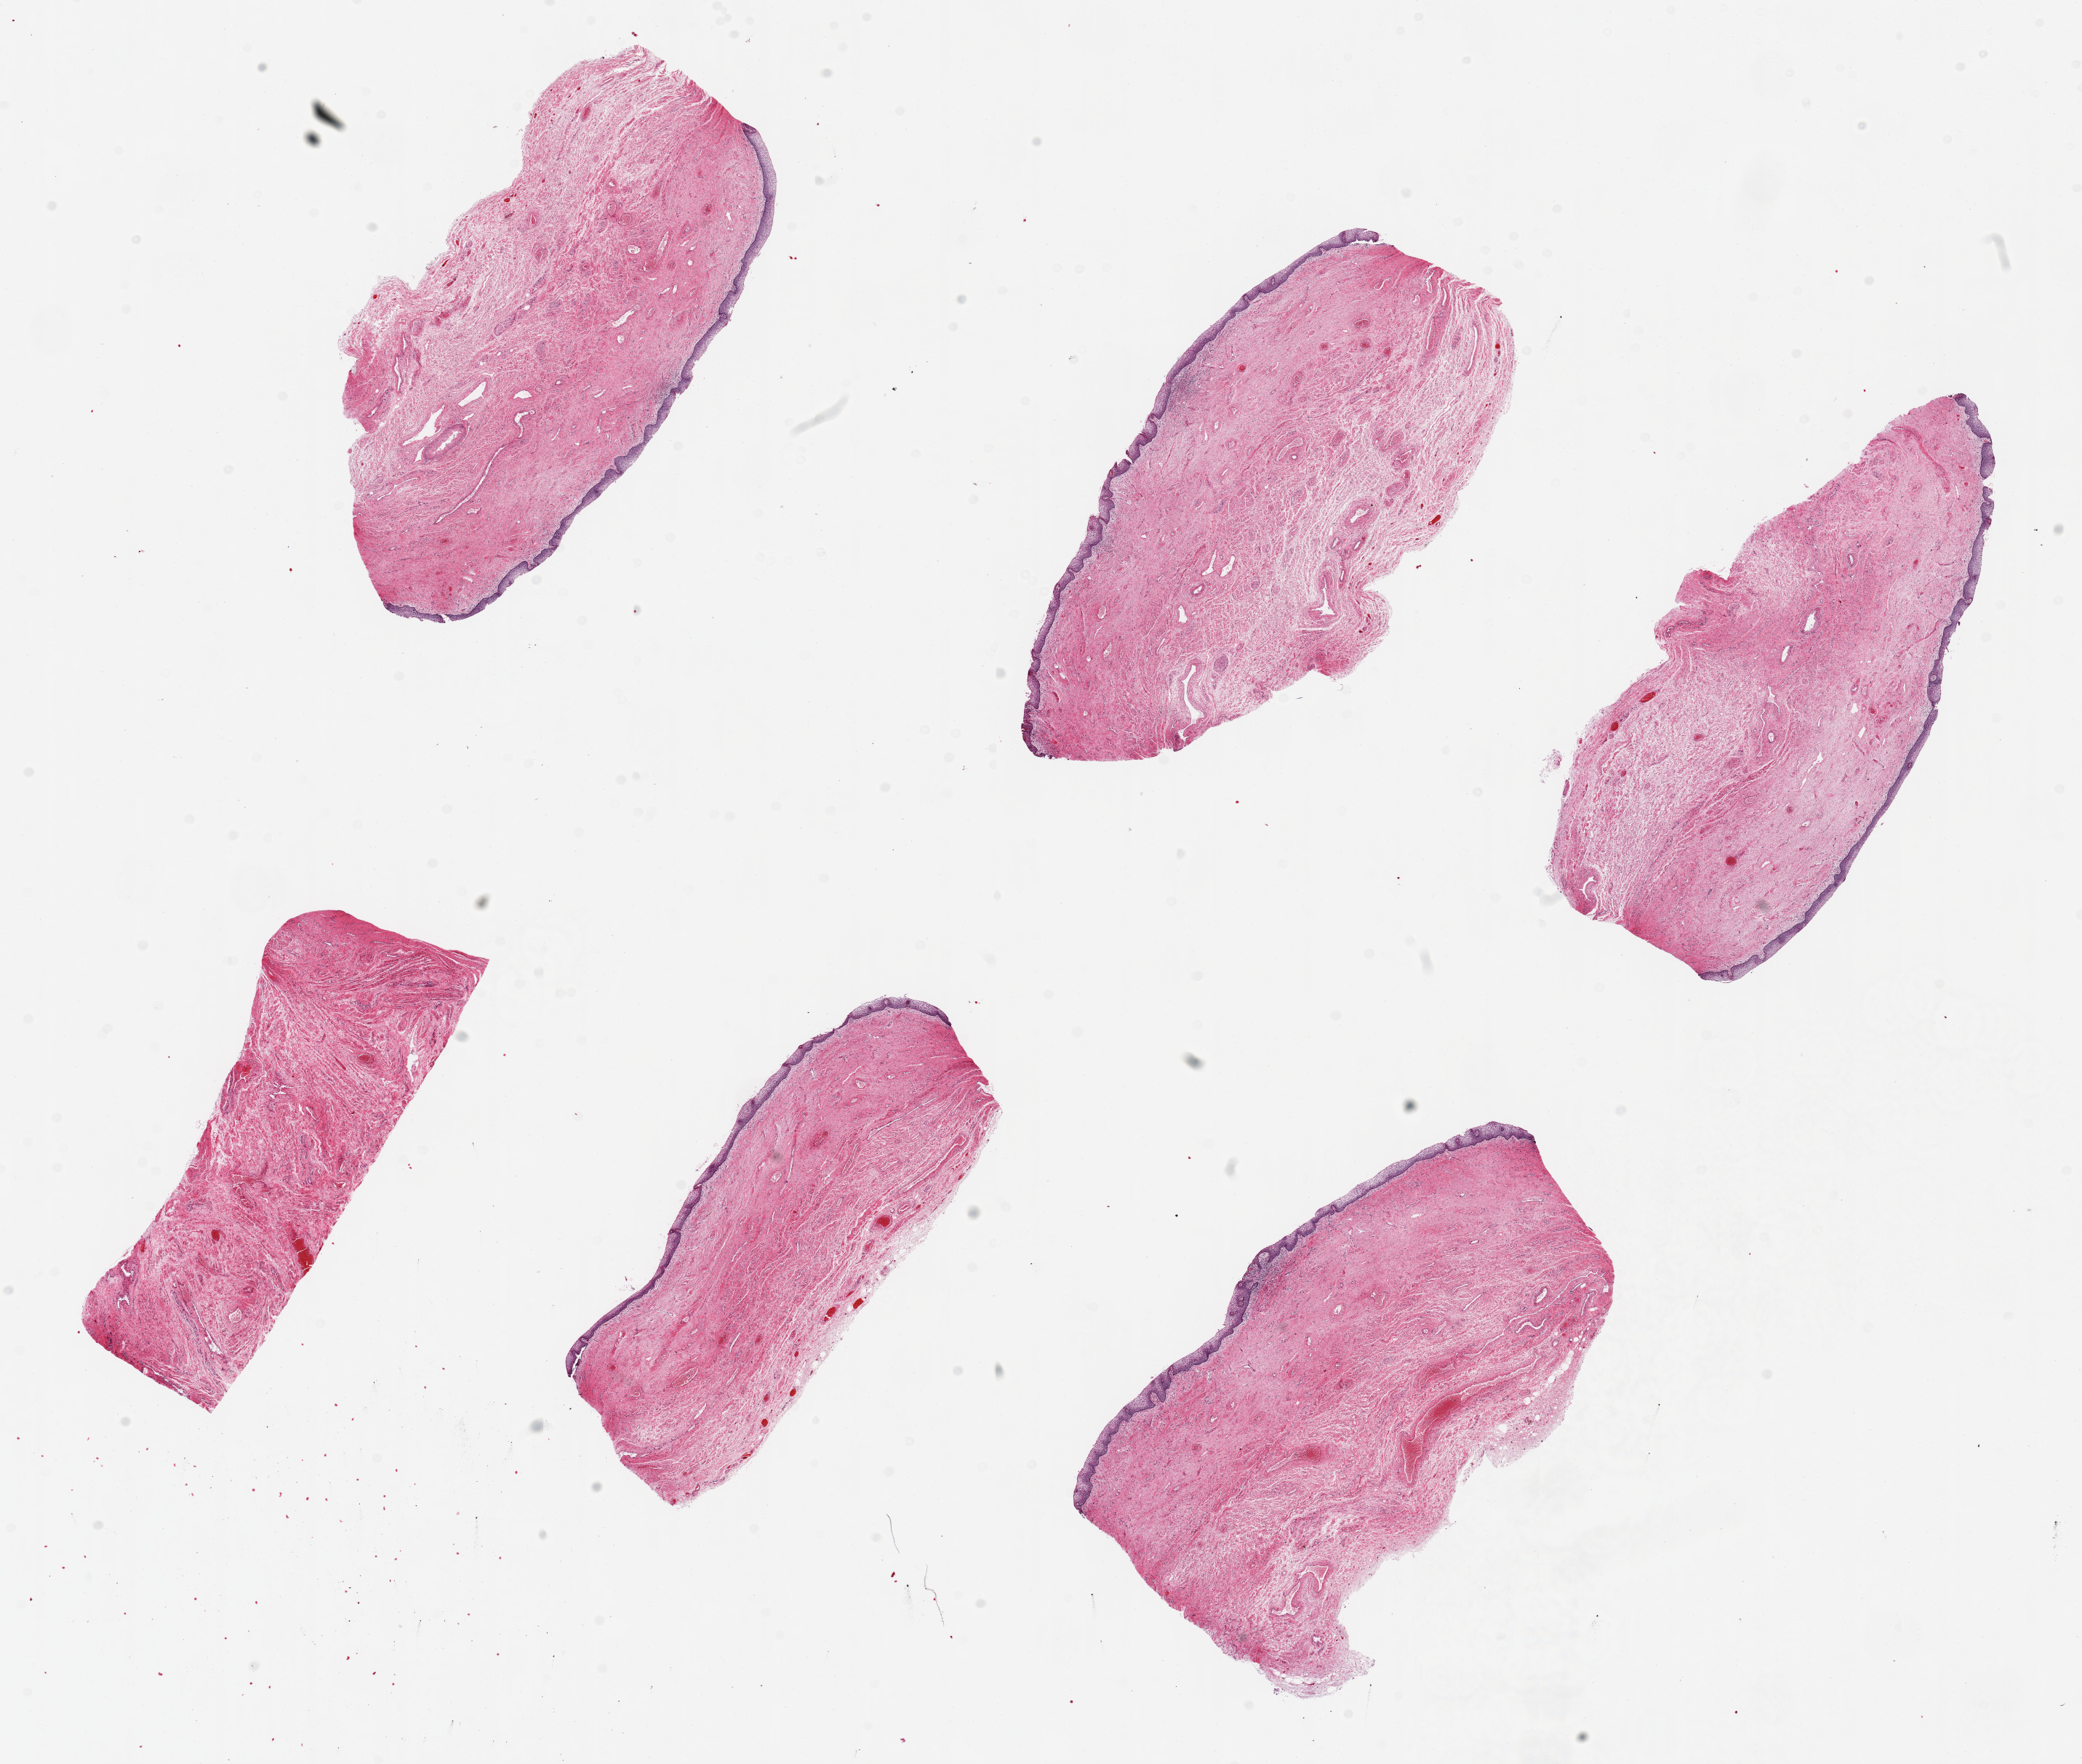
Haematoxylin and eosin whole-slide image — low-resolution overview of the scanned area, about 22.6 x 19.2 mm, PAXgene-fixed, paraffin-embedded tissue, target tissue: vagina, tissue donor sample.
Reviewer comment on this tissue sample: 6 pieces, up to 7x3mm; 1 of 6 without epithelium.